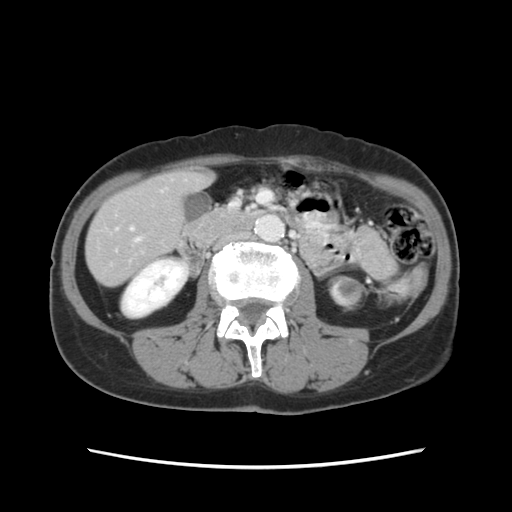
Contrast-enhanced abdominal CT, one axial slice; 120 kVp; intravenous contrast given; soft-tissue window (W 400 / L 40 HU); 2.5 mm slice thickness; 512 × 512 image matrix. Female patient, age 70 years. From the clinical record (not read from this slice): diagnosis: colorectal cancer liver metastases, imaged before liver resection; multiple liver metastases: no; largest metastasis: 2.5 cm; chemotherapy before resection: yes.
Outlined on this slice (expert manual segmentation):
- hepatic veins: bounding box (x1, y1, x2, y2) in pixels: (135, 238, 140, 242)
- liver: (87, 171, 209, 285)
- planned liver remnant (the part of the liver to remain after resection): (87, 171, 207, 286)
- portal vein (with intrahepatic branches): (130, 227, 133, 231)